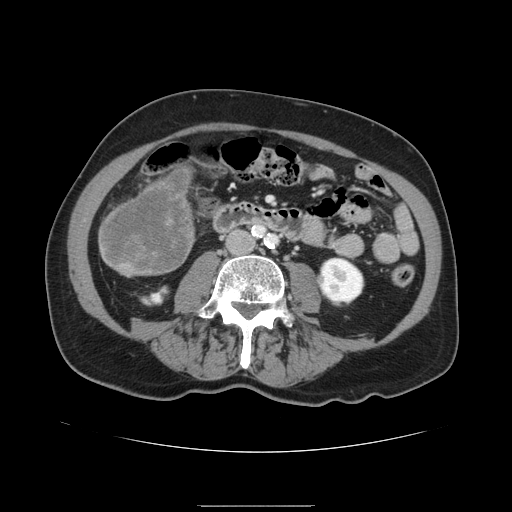
Contrast-enhanced abdominal CT, one axial slice; slice 26 of 168 in the series (ordered by position); intravenous contrast given; soft-tissue window (W 400 / L 40 HU); 512 × 512 image matrix, field of view 386 × 386 mm. Male patient, age 74 years. Case-level facts recorded for this patient, not image findings: diagnosis: colorectal cancer liver metastases, imaged before liver resection; multiple liver metastases: no; largest metastasis: 14.5 cm; disease in both lobes: yes.
Annotated regions visible in this slice (expert manual segmentation):
- liver: bounding box <98,169,195,276> (left, top, right, bottom; pixels)
- liver metastasis: <101,173,191,272>